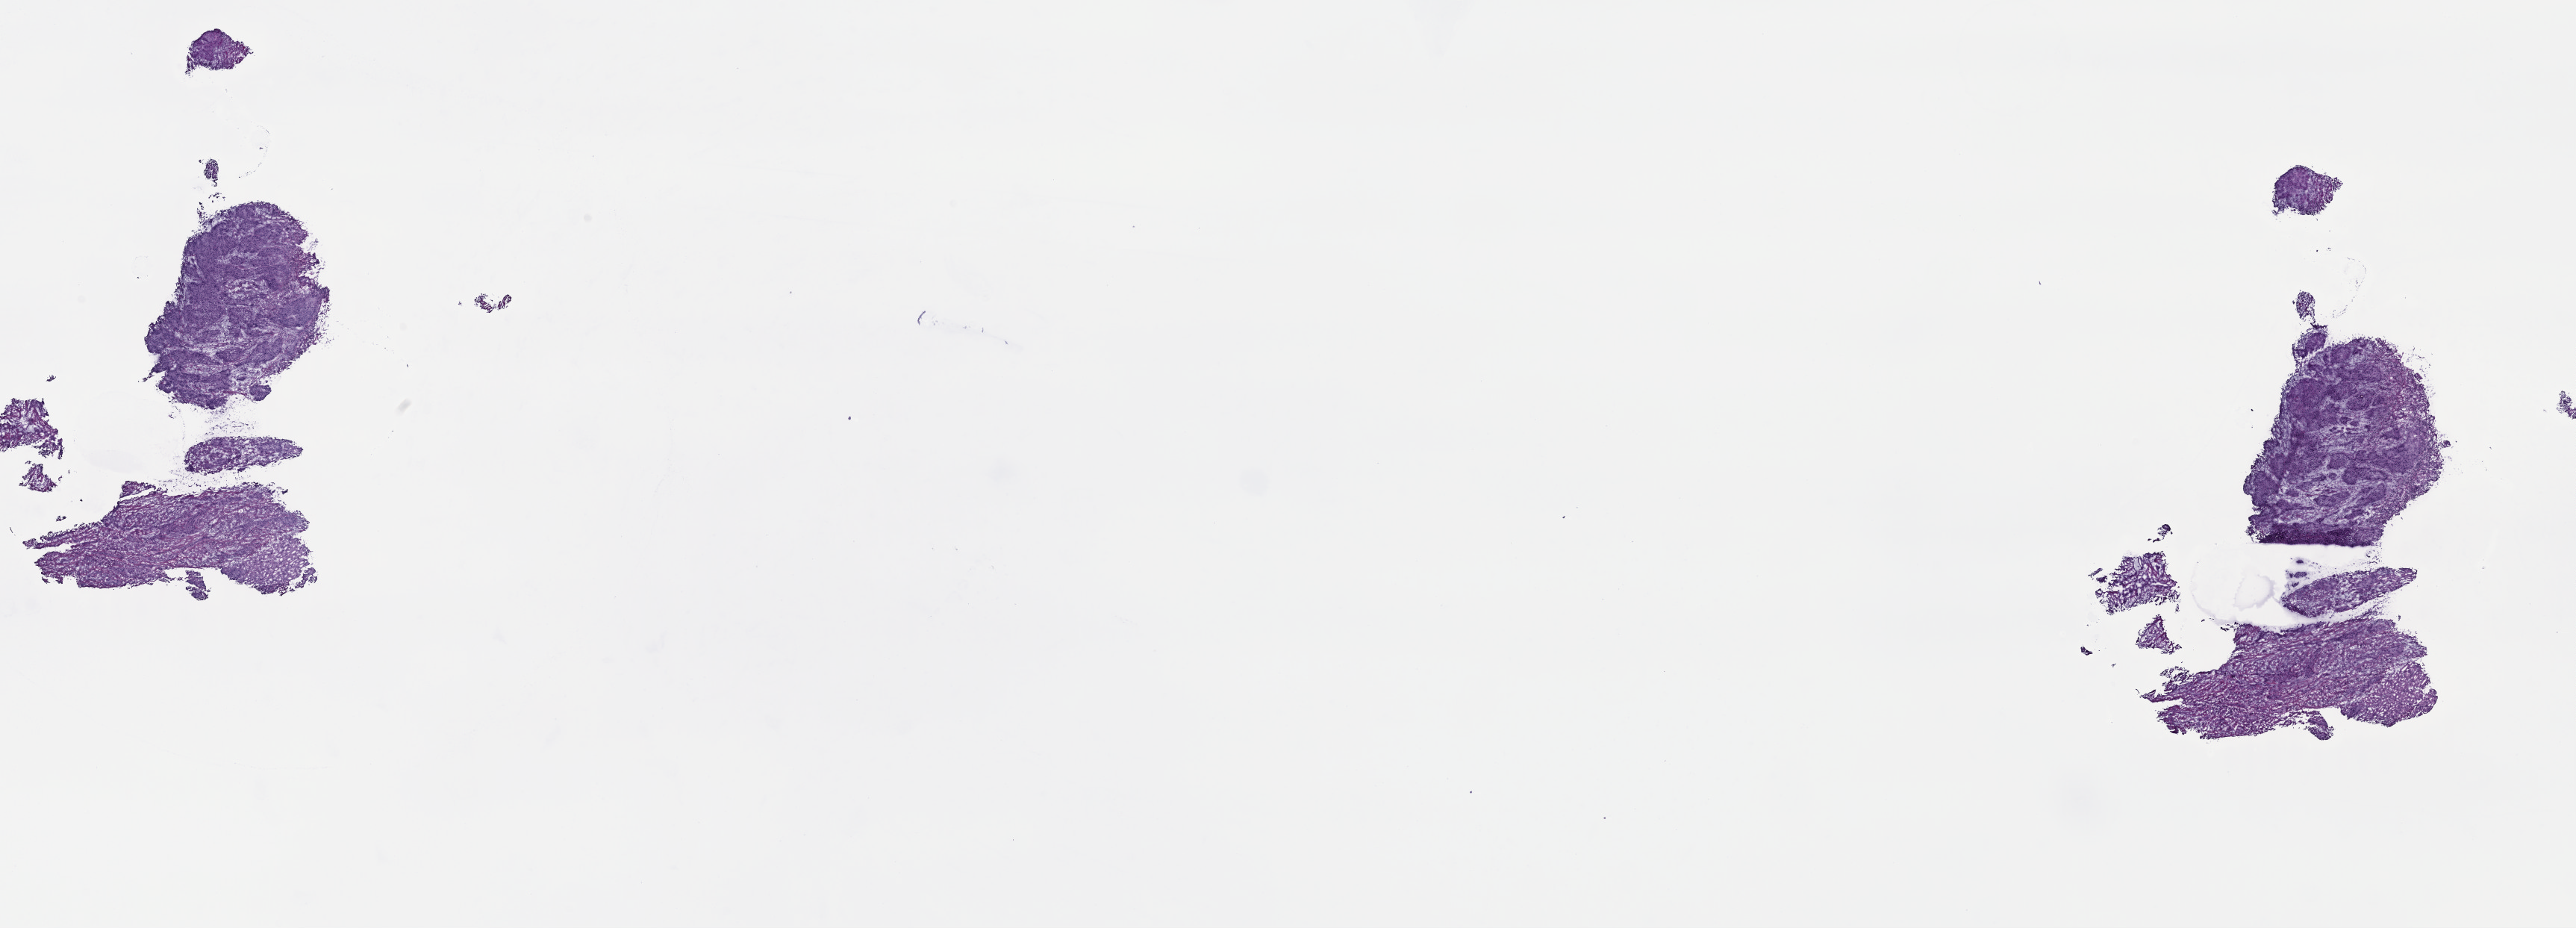
Hematoxylin and eosin (H&E) stained whole-slide image — a low-resolution overview of the entire scanned area, about 27.1 x 9.8 mm (from a 40x scan); frozen section from the top of the tissue portion; primary tumour sample from the head and neck. Female, age 61 years at initial diagnosis. Histologic grade: G2 (moderately differentiated). Slide review estimates, as recorded: tumour cells 60%, tumour nuclei 70%, normal cells 0%, stromal cells 30%, necrosis 10%. Inflammatory infiltration, as recorded: lymphocyte infiltration 50%, monocyte infiltration 0%, neutrophil infiltration 50%.
TNM: T4b N0 M0. AJCC pathologic stage: IVB. Histologic diagnosis: Squamous cell carcinoma, NOS (tongue, NOS).